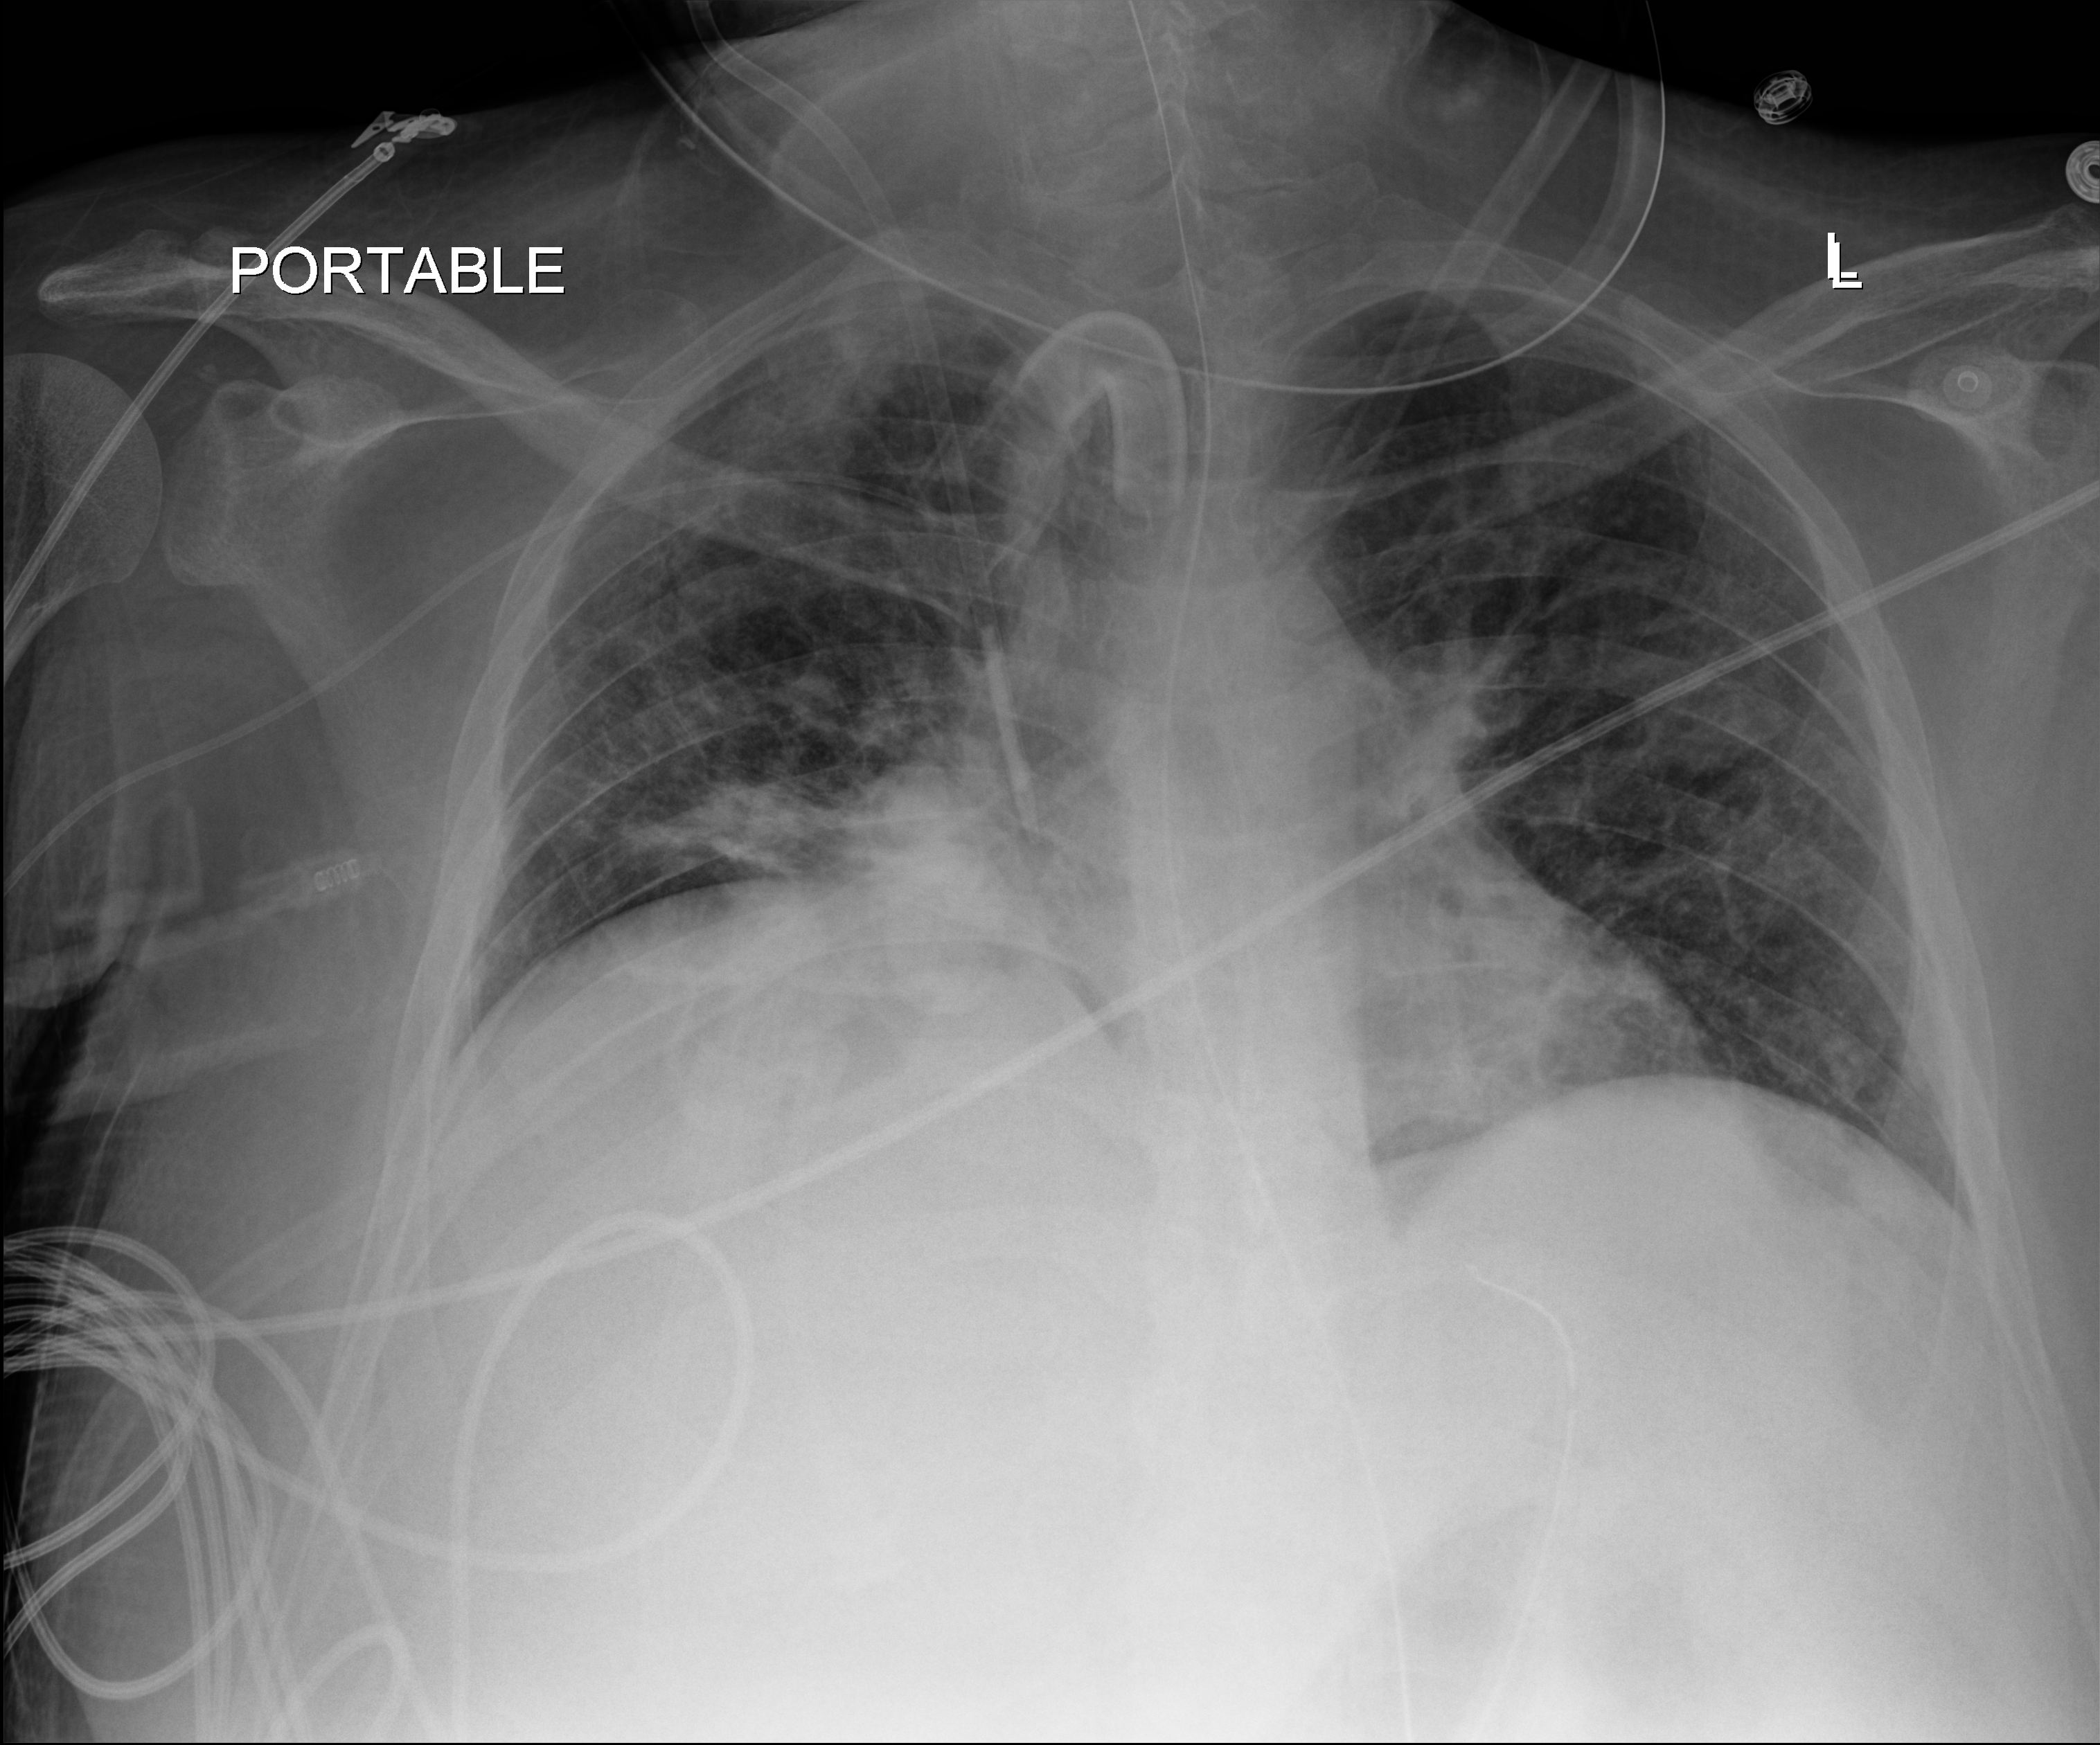
Portable chest radiograph; anteroposterior (AP) projection. Patient hospitalised with COVID-19, aged 18–59 years.
Admission-level facts for this patient (not findings on this image; timing relative to this image not recorded):
- COPD (admission record): no
- chronic kidney disease (admission record): no